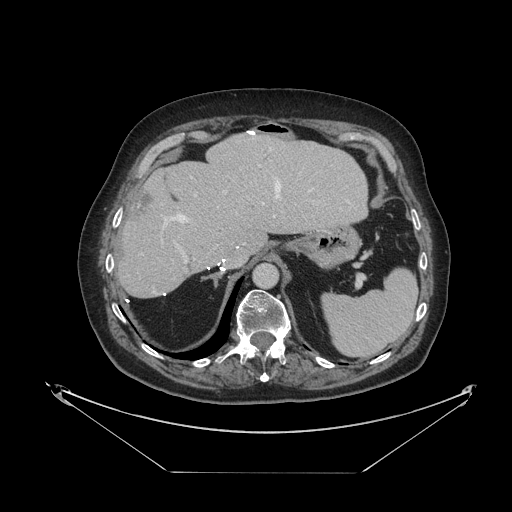
Contrast-enhanced abdominal CT, one axial slice. Slice 77 of 121 in the series (ordered by position). Intravenous contrast given. Soft-tissue window (W 400 / L 40 HU). 2.5 mm slice thickness. 512 × 512 image matrix. Male patient, age 68 years. Case-level facts recorded for this patient, not image findings: diagnosis: colorectal cancer liver metastases, imaged before liver resection; multiple liver metastases: no; largest metastasis: 4 cm; disease in both lobes: no.
Outlined on this slice (manually delineated by an expert):
- hepatic veins: bounding box [x1, y1, x2, y2] px = [162, 148, 349, 230]
- liver: [119, 135, 367, 297]
- planned liver remnant (the part of the liver to remain after resection): [119, 135, 368, 297]
- portal vein (with intrahepatic branches): [176, 165, 314, 264]
- liver metastasis: [133, 192, 152, 217]